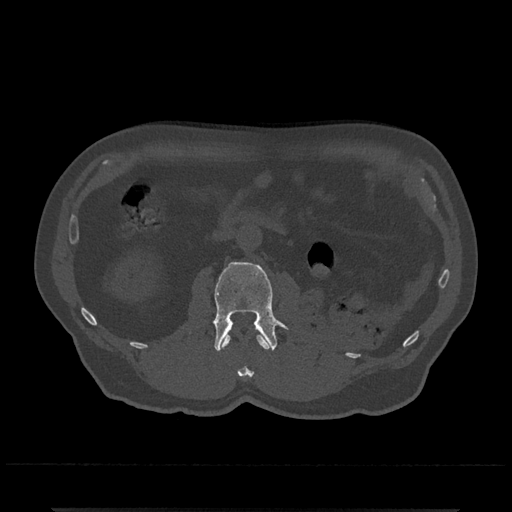
CT including the spine, one axial slice. Slice 307 of 797 in the series (ordered by position). Reconstruction kernel Br40s/3. 120 kVp. Bone window (W 1800 / L 400 HU). 0.5 mm slice thickness. 512 × 512 image matrix, field of view 393 × 393 mm. Male patient, age 67 years. Case-level facts recorded for this patient, not image findings: primary cancer: prostate.
Annotated regions visible in this slice (semi-automatic segmentation, software-assisted and operator-edited):
- L1 vertebra: bounding box [x1, y1, x2, y2] px = [221, 333, 269, 377]
- L2 vertebra: [213, 261, 288, 351]